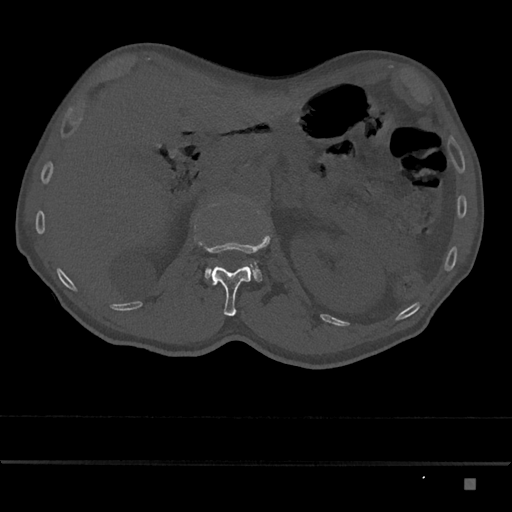
CT including the spine, one axial slice; position 526 of 797 along the scan axis; 120 kVp; bone window (W 1800 / L 400 HU); 0.5 mm slice thickness; 512 × 512 image matrix, field of view 390 × 390 mm. Patient: male, 72 years. Case-level facts recorded for this patient, not image findings: primary cancer: prostate.
Structures marked on this image (semi-automatically segmented with operator editing):
- L1 vertebra: bounding box [x1, y1, x2, y2] px = [200, 236, 270, 316]
- L2 vertebra: [198, 243, 263, 282]